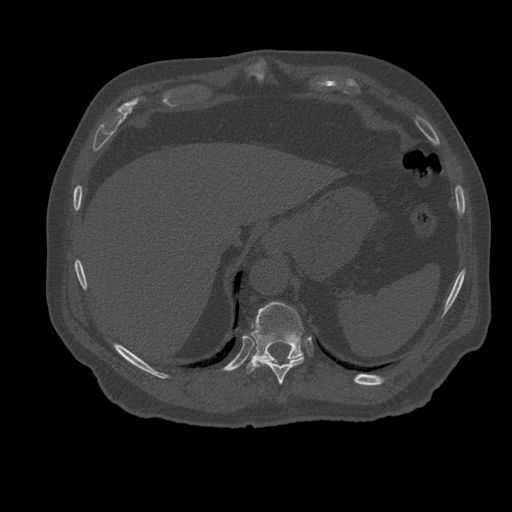
CT including the spine, one axial slice; position 291 of 399 along the scan axis; reconstruction kernel STANDARD; bone window (W 1800 / L 400 HU); 1.25 mm slice thickness; 512 × 512 image matrix, field of view 407 × 407 mm. Patient age 73 years. Case-level facts recorded for this patient, not image findings: primary cancer: prostate; vertebrae with lytic lesions (as recorded): L2.
Outlined on this slice (semi-automatic segmentation, software-assisted and operator-edited):
- T10 vertebra: bounding box (x1, y1, x2, y2) in pixels: (256, 356, 304, 385)
- T11 vertebra: (246, 302, 304, 374)